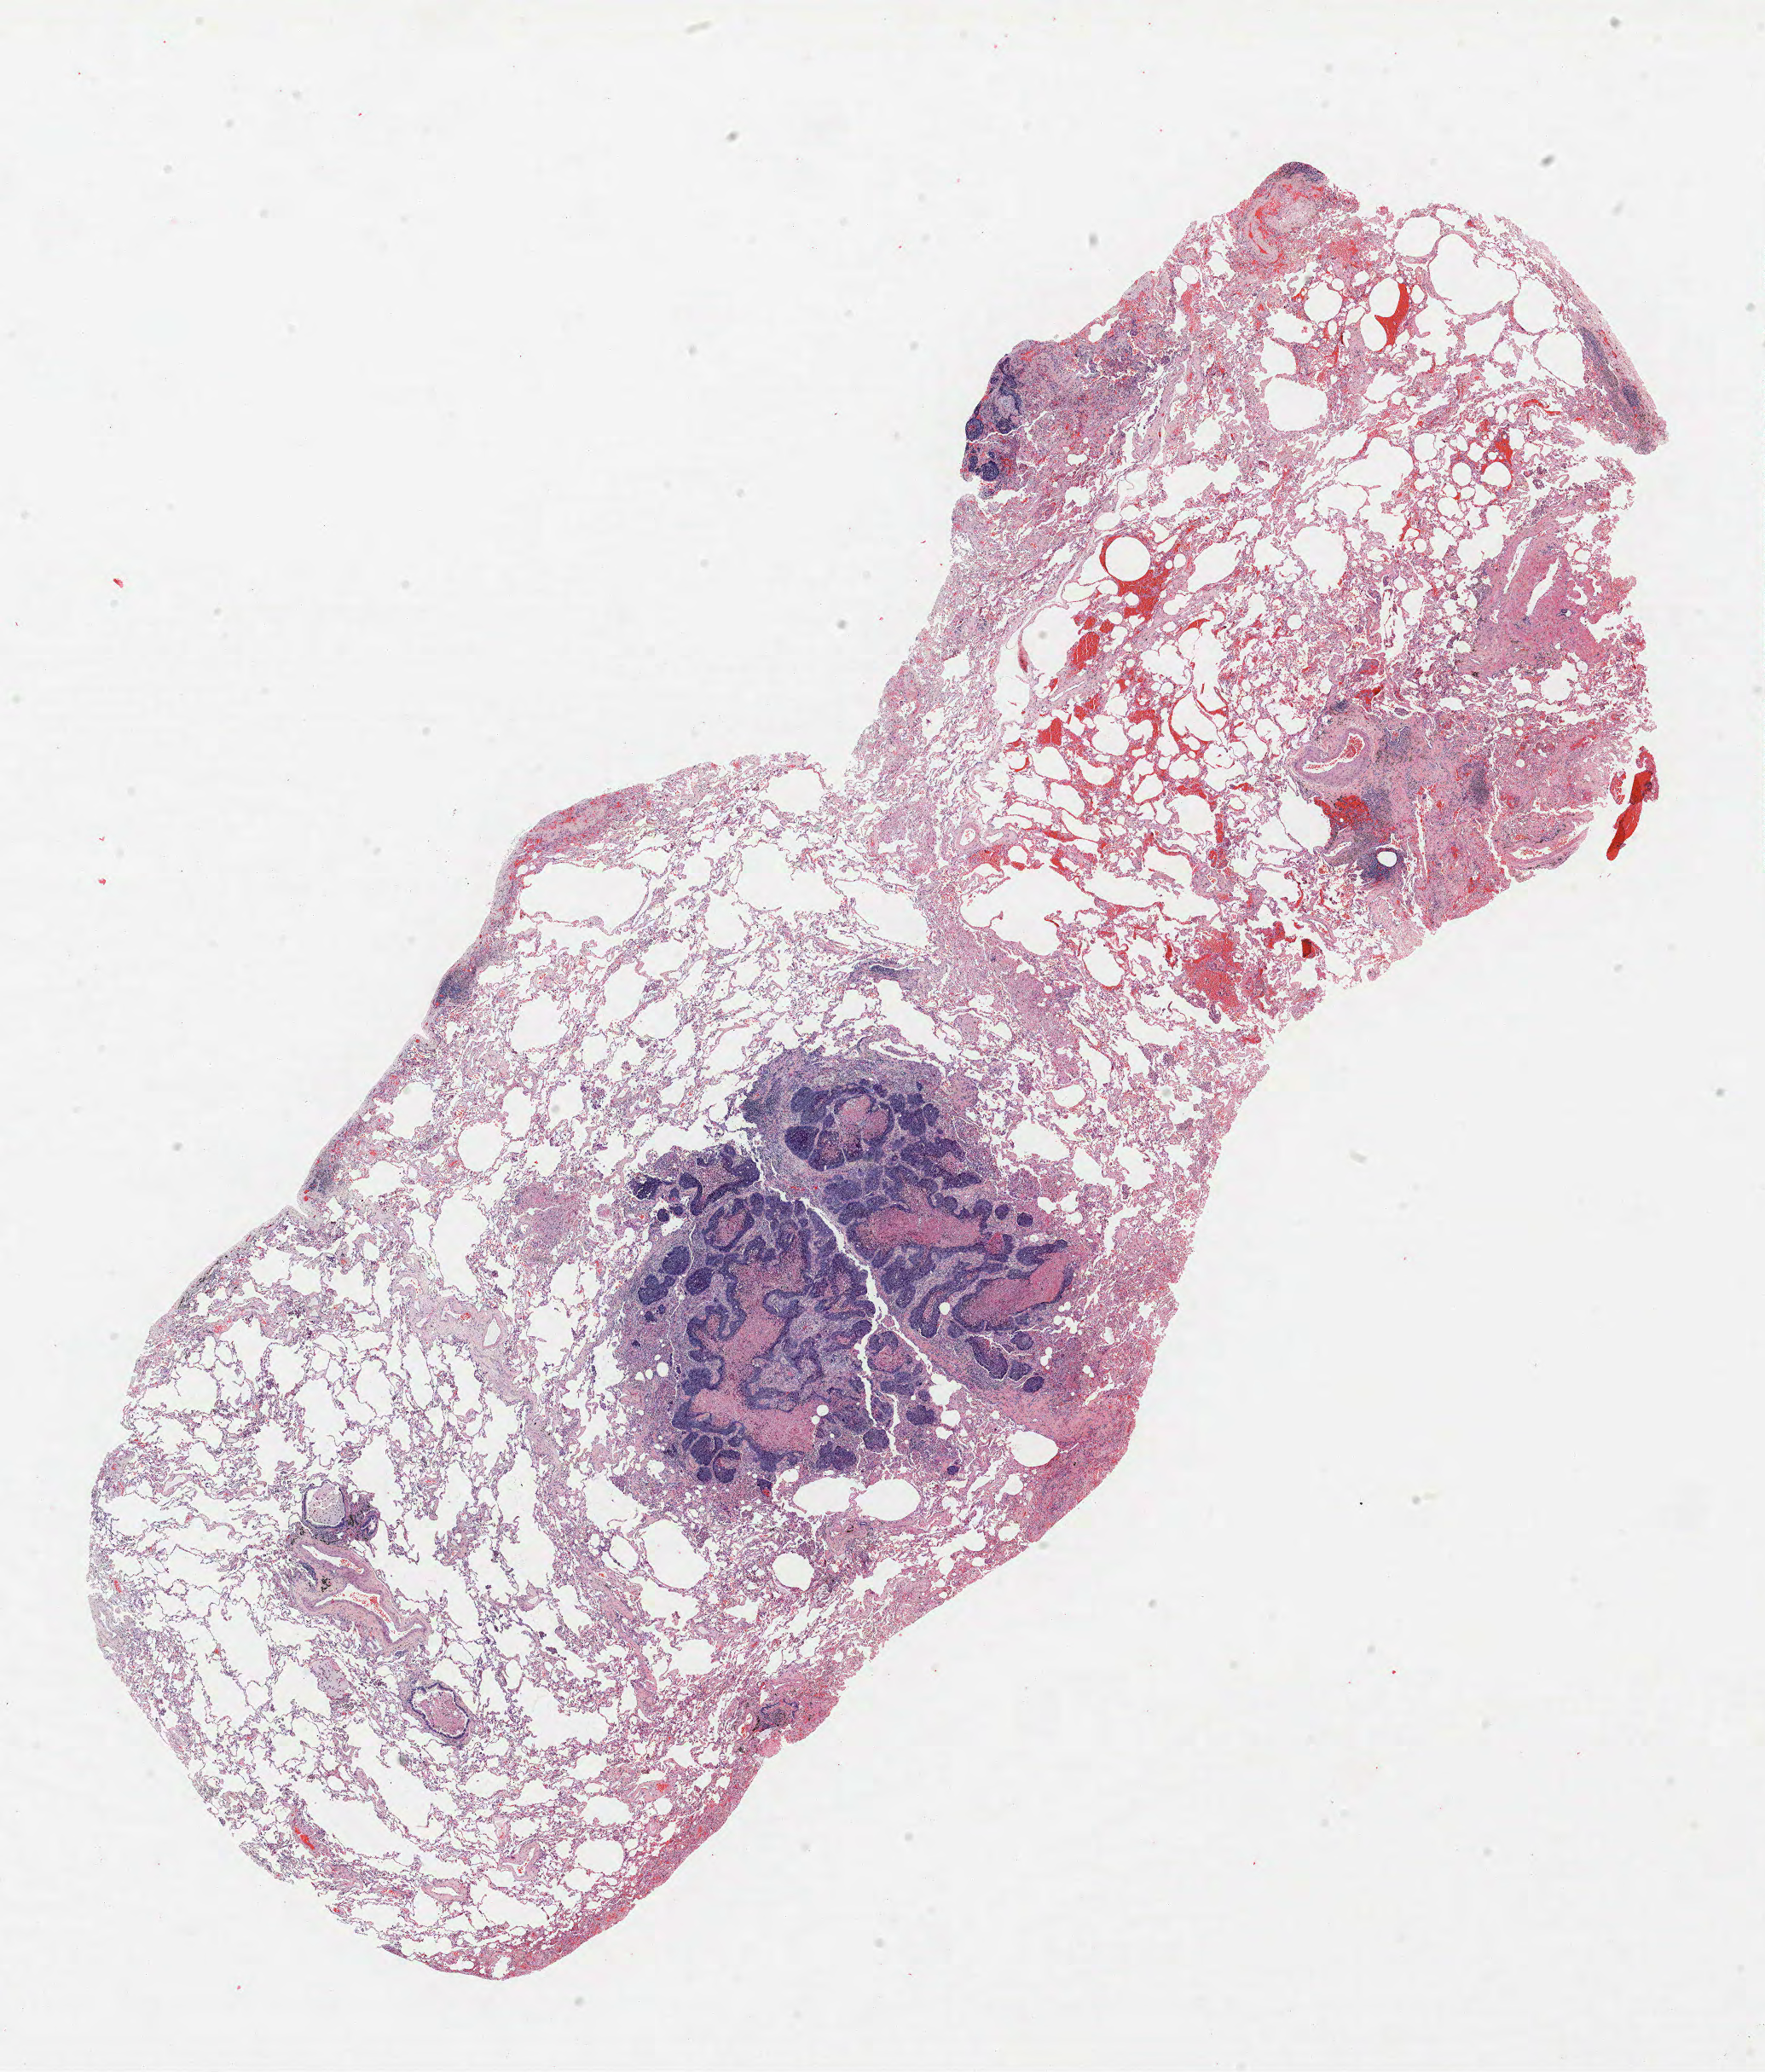
Whole-slide histology image, H&E-stained, low-resolution overview of the scanned area, about 16.6 x 19.4 mm; formalin-fixed paraffin-embedded (FFPE) section; lung. Male patient, aged 61 at enrolment. Current smoker at enrolment.
Participant's lung-cancer diagnosis: Squamous cell carcinoma, NOS.